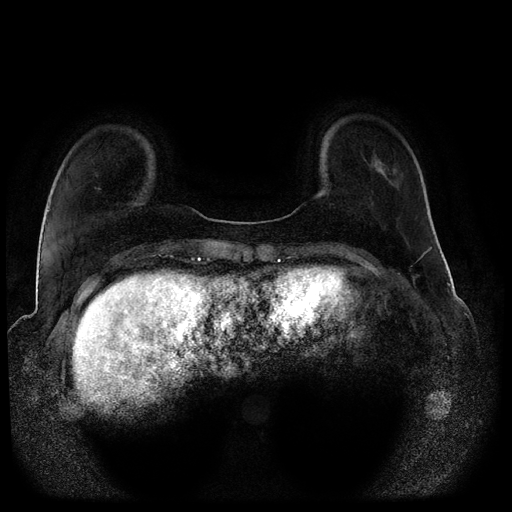
Breast MRI (dynamic contrast-enhanced, multi-phase), one axial slice. Slice 26 of 116 in the series (ordered by position). Dynamic contrast-enhanced series, time point 2 of 5 at this slice position (early post-contrast). 1.5 T. TE 2.6 ms, TR 5.3 ms. 2 mm slice thickness. 512 × 512 image matrix, field of view 370 × 370 mm. Female patient, age 44 years.
Annotated regions visible in this slice (semi-automatic segmentation, software-assisted and operator-edited):
- breast lesion (labelled benign in the annotation): bounding box <374,160,385,176> (left, top, right, bottom; pixels)